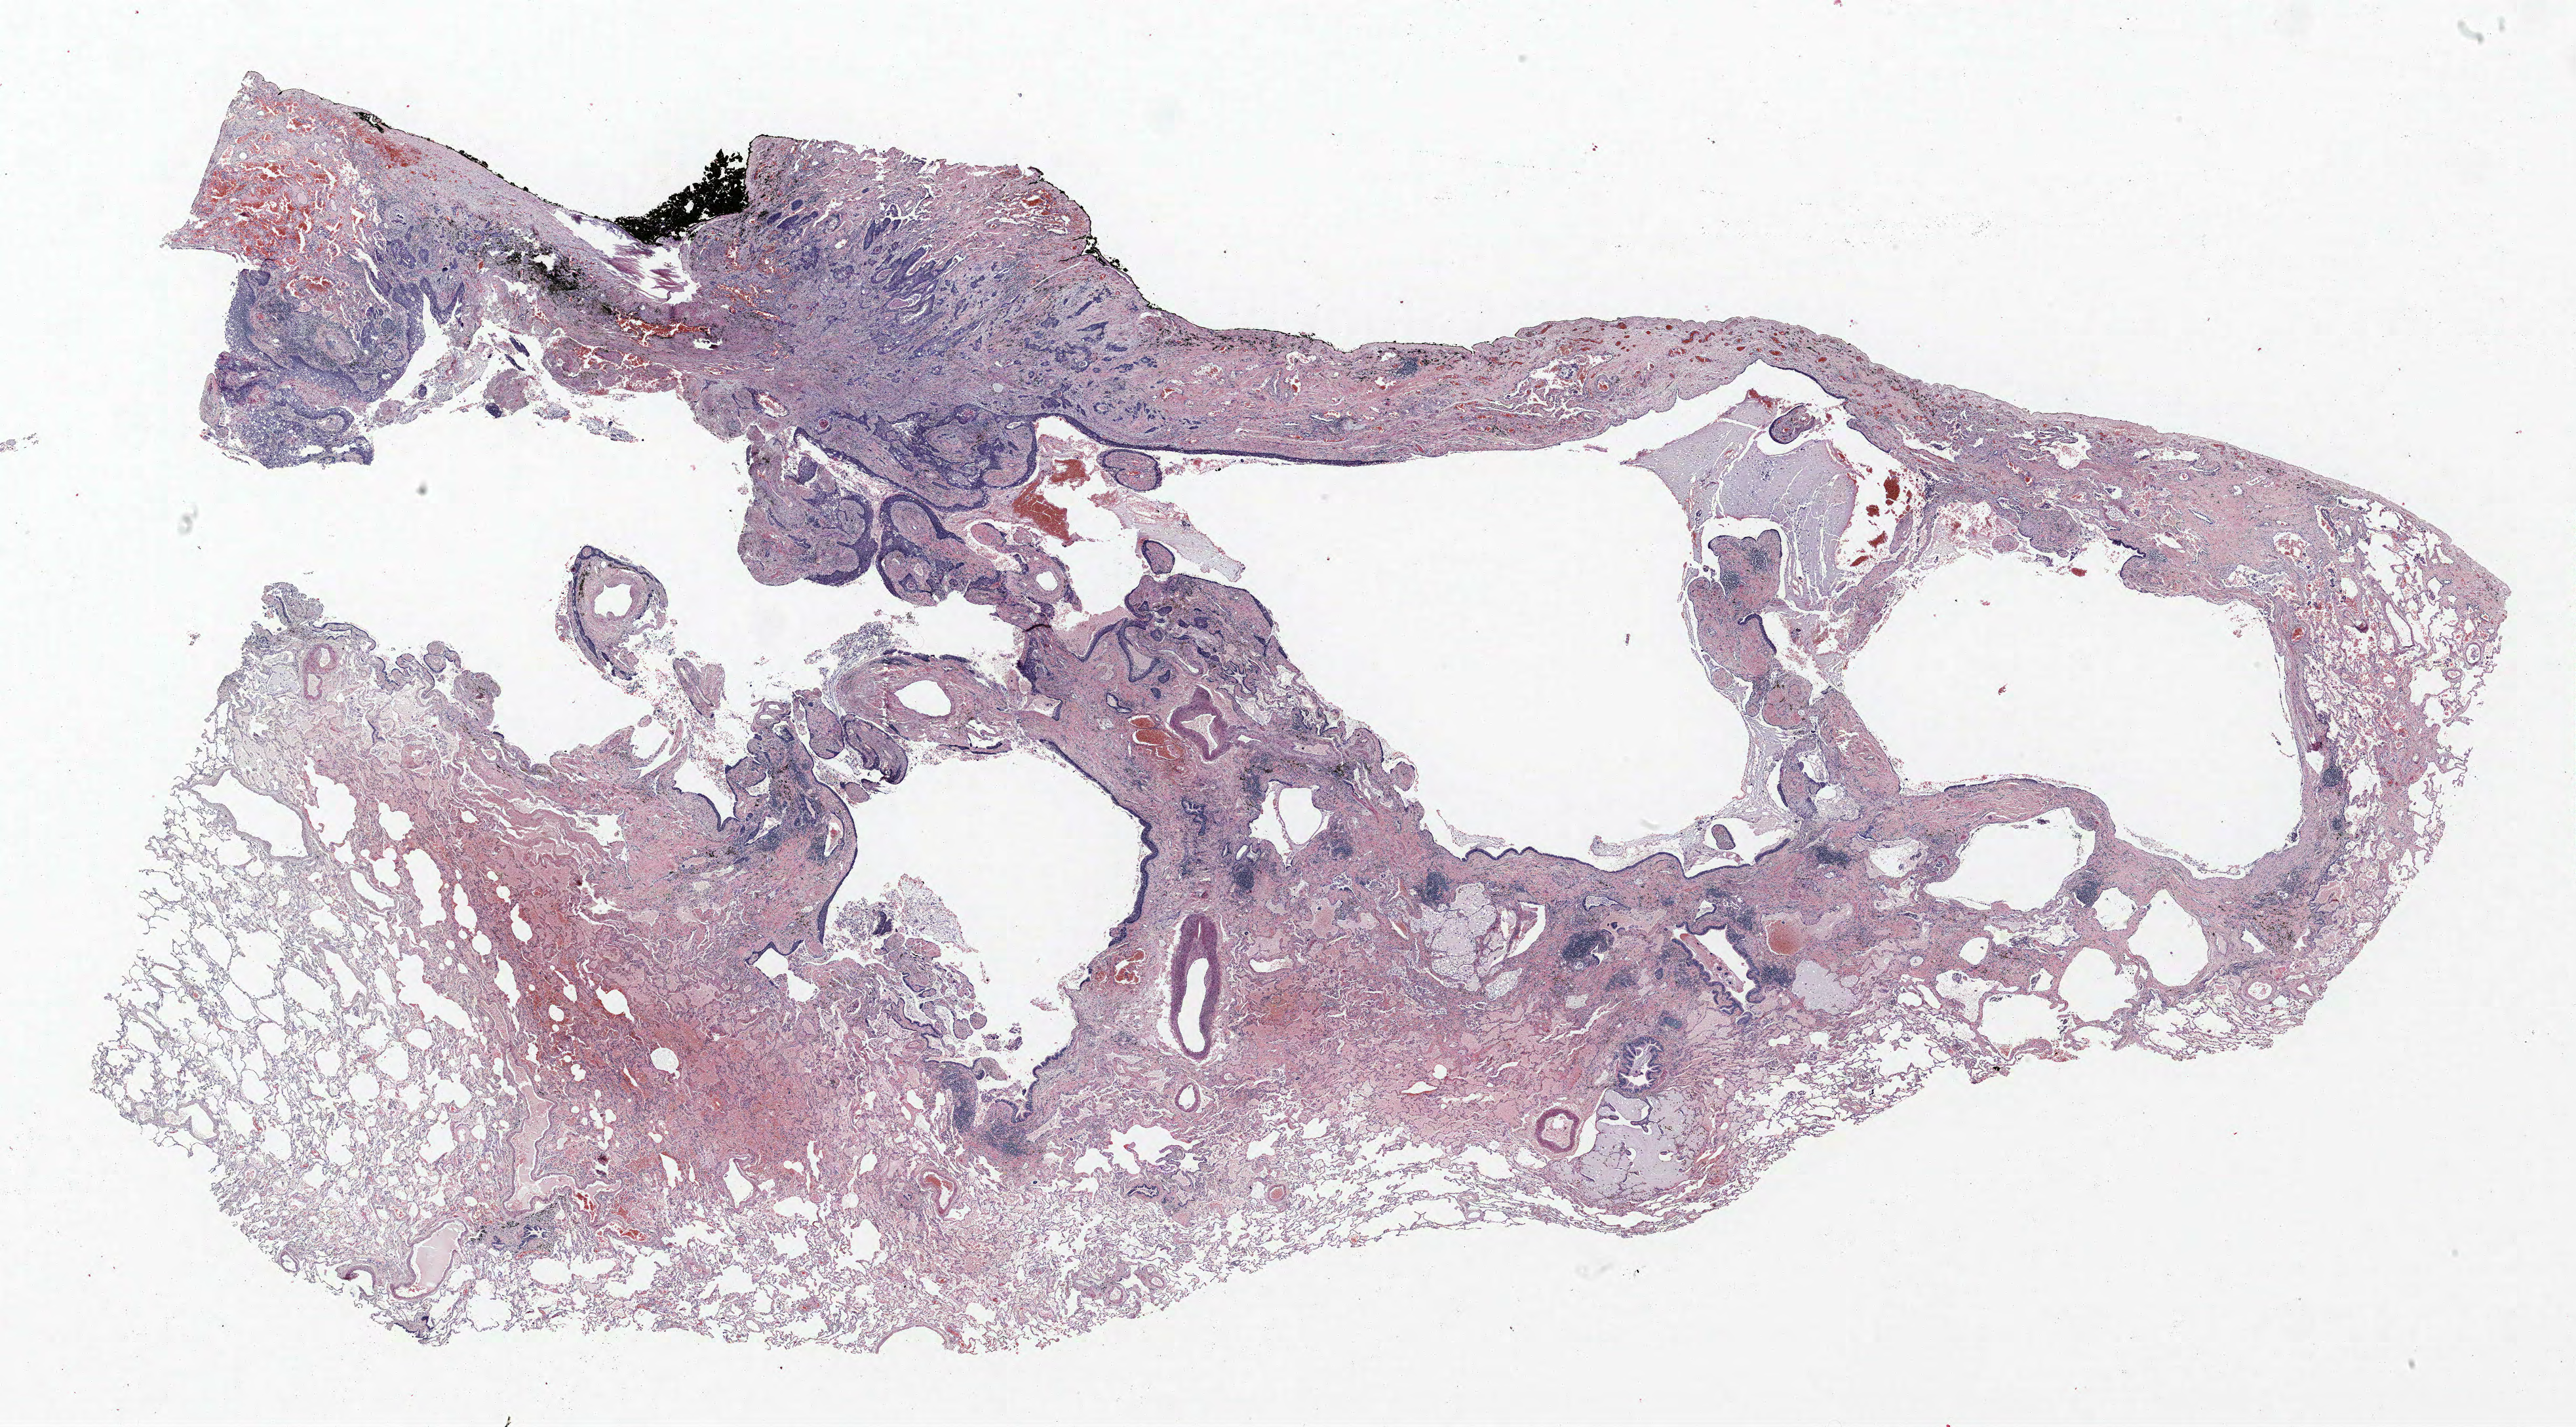
Hematoxylin and eosin (H&E) stained whole-slide image — whole scanned area (about 31.4 x 17.4 mm) shown as a low-resolution overview, formalin-fixed paraffin-embedded (FFPE) section, lung tissue. Male, age 55 at enrolment. Grade: moderately differentiated (G2).
- tumour size (pathology): 75 mm
- stage (AJCC 6th edition): IB
- participant's lung-cancer diagnosis: Adenocarcinoma, NOS
- primary tumour location (clinical record): right lower lobe
- note: participant had 2 primary lung cancers recorded; fields above describe the first